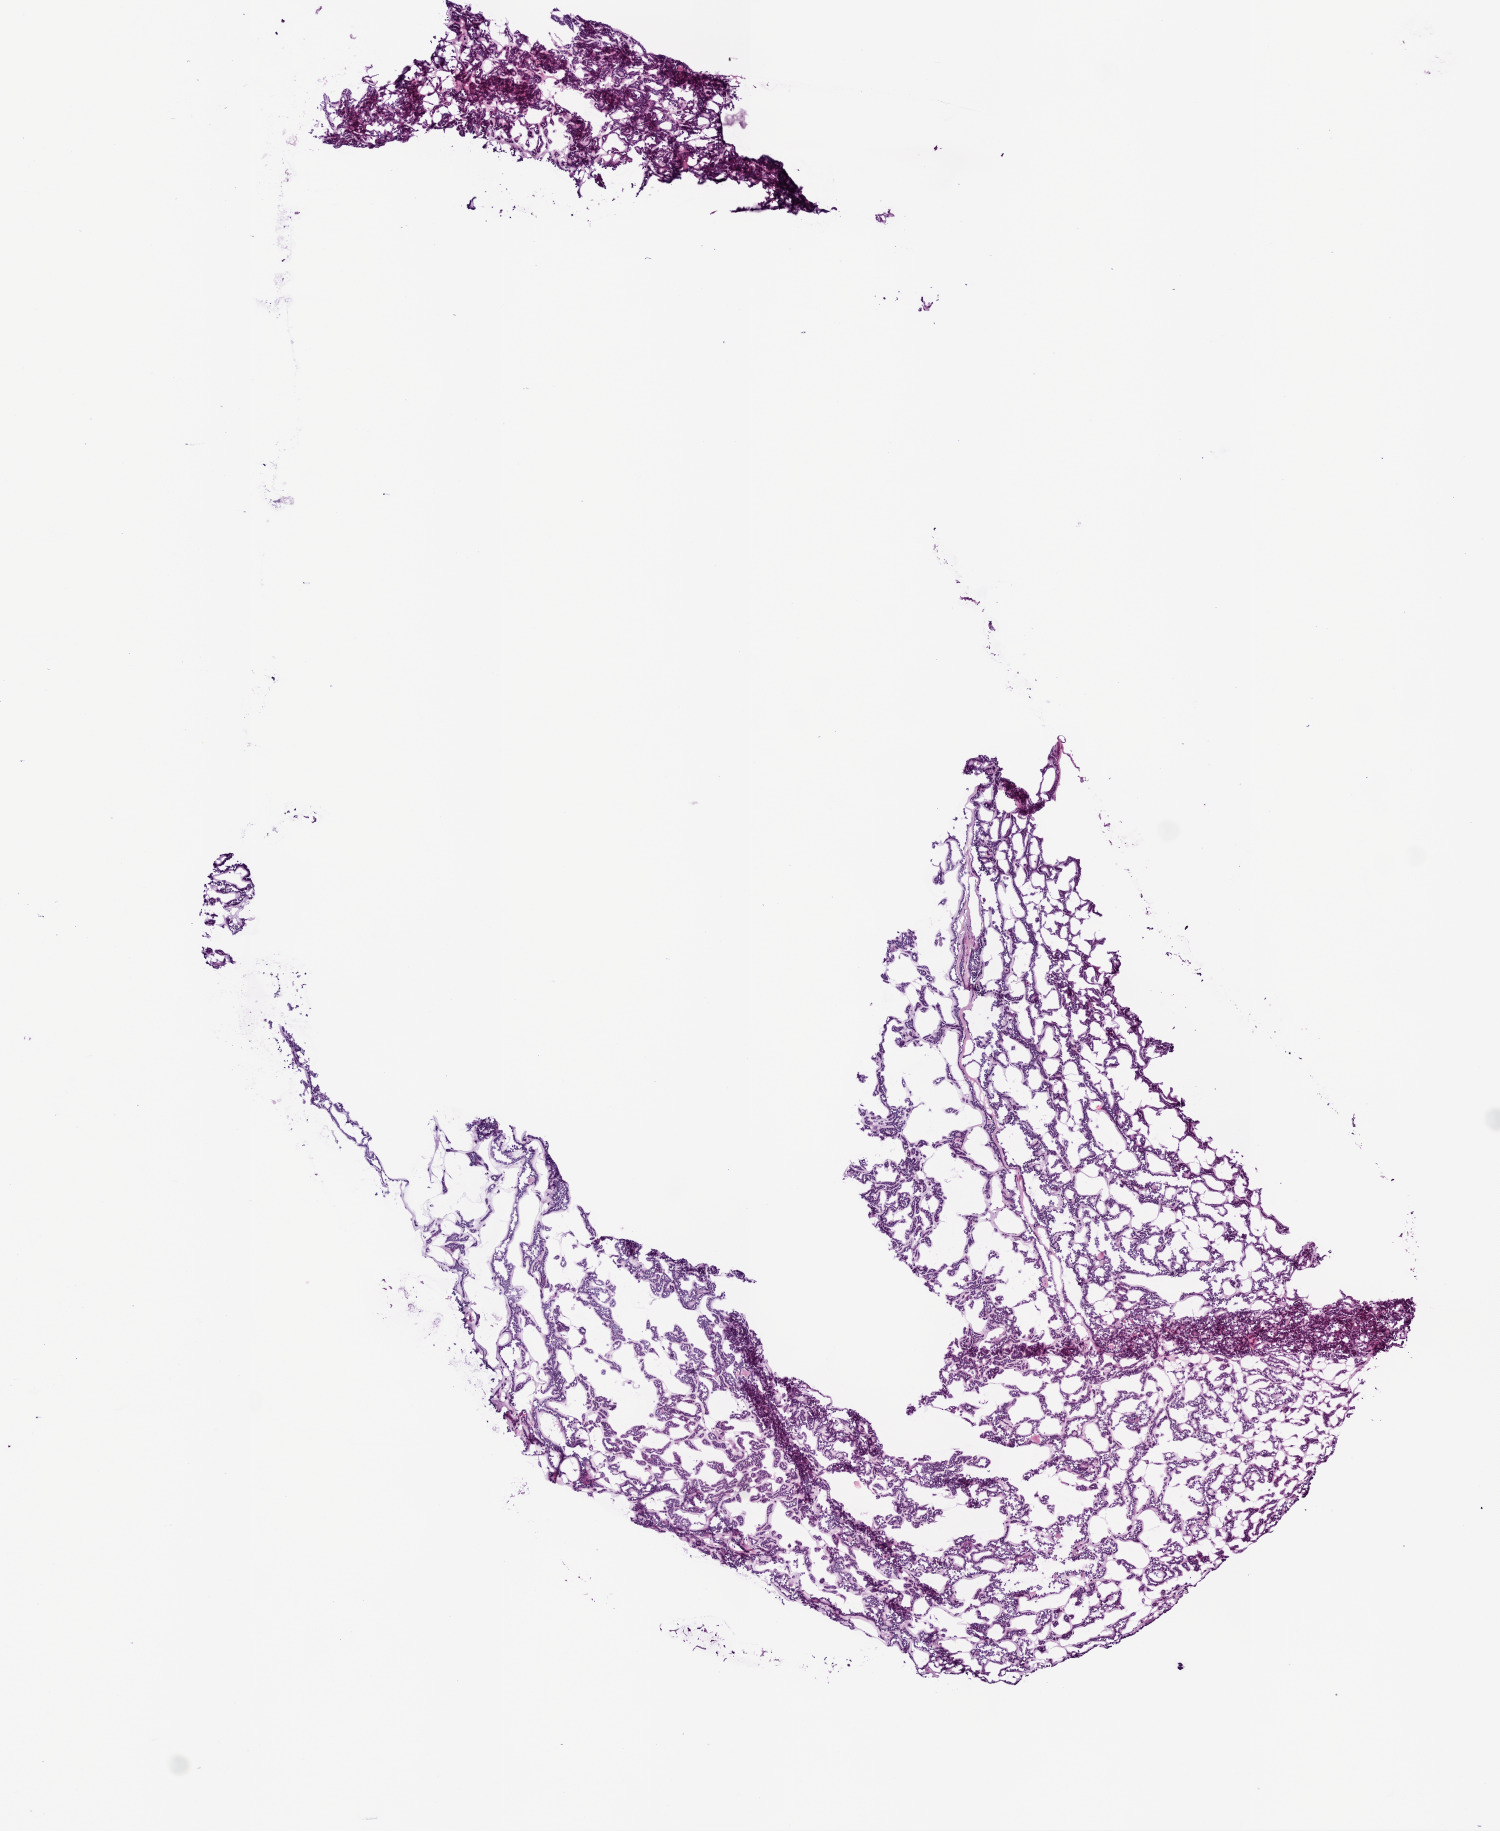
Whole-slide histology image, Hematoxylin and eosin (H&E) stained — low-resolution overview of the scanned area, about 6.0 x 7.3 mm (from a 20x scan). Frozen section from the bottom of the tissue portion. Sample: primary tumour, kidney. Female, age 54 years at initial diagnosis. Slide review estimates, as recorded: tumour cells 98%, tumour nuclei 80%, normal cells 0%, stromal cells 2%, necrosis 0%.
- pathologic diagnosis: Papillary adenocarcinoma, NOS